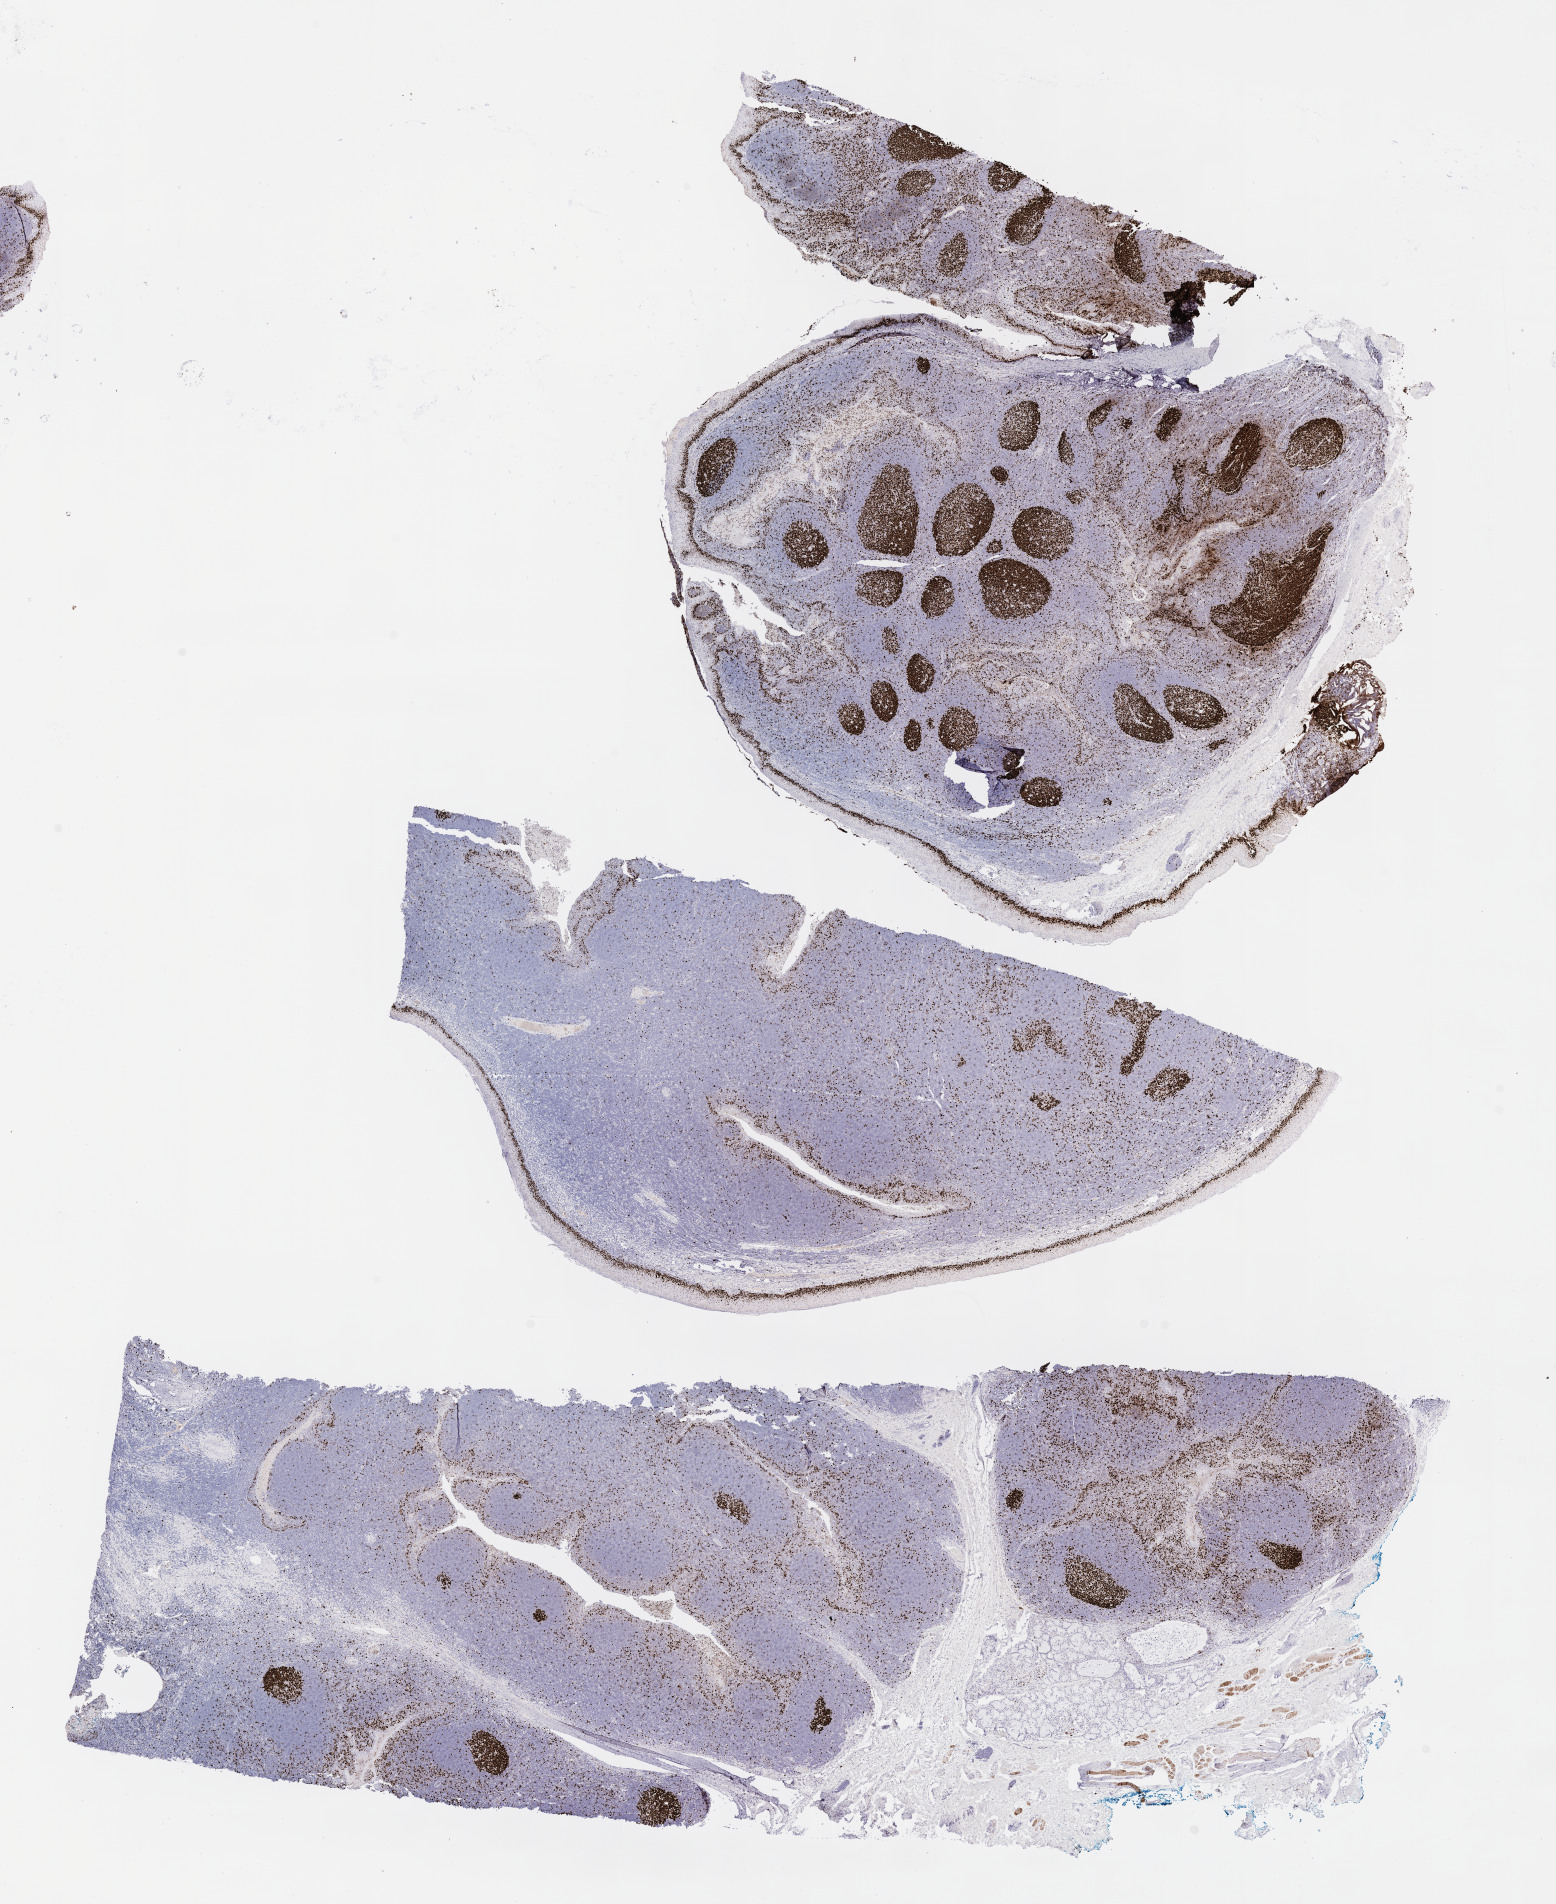
Whole-slide image, immunohistochemical stain for Ki-67, a low-resolution overview of the entire scanned area, about 12.6 x 15.4 mm, specimen: tumor tissue. Female, age 8 years at initial diagnosis.
Diagnosis: Burkitt lymphoma, NOS.